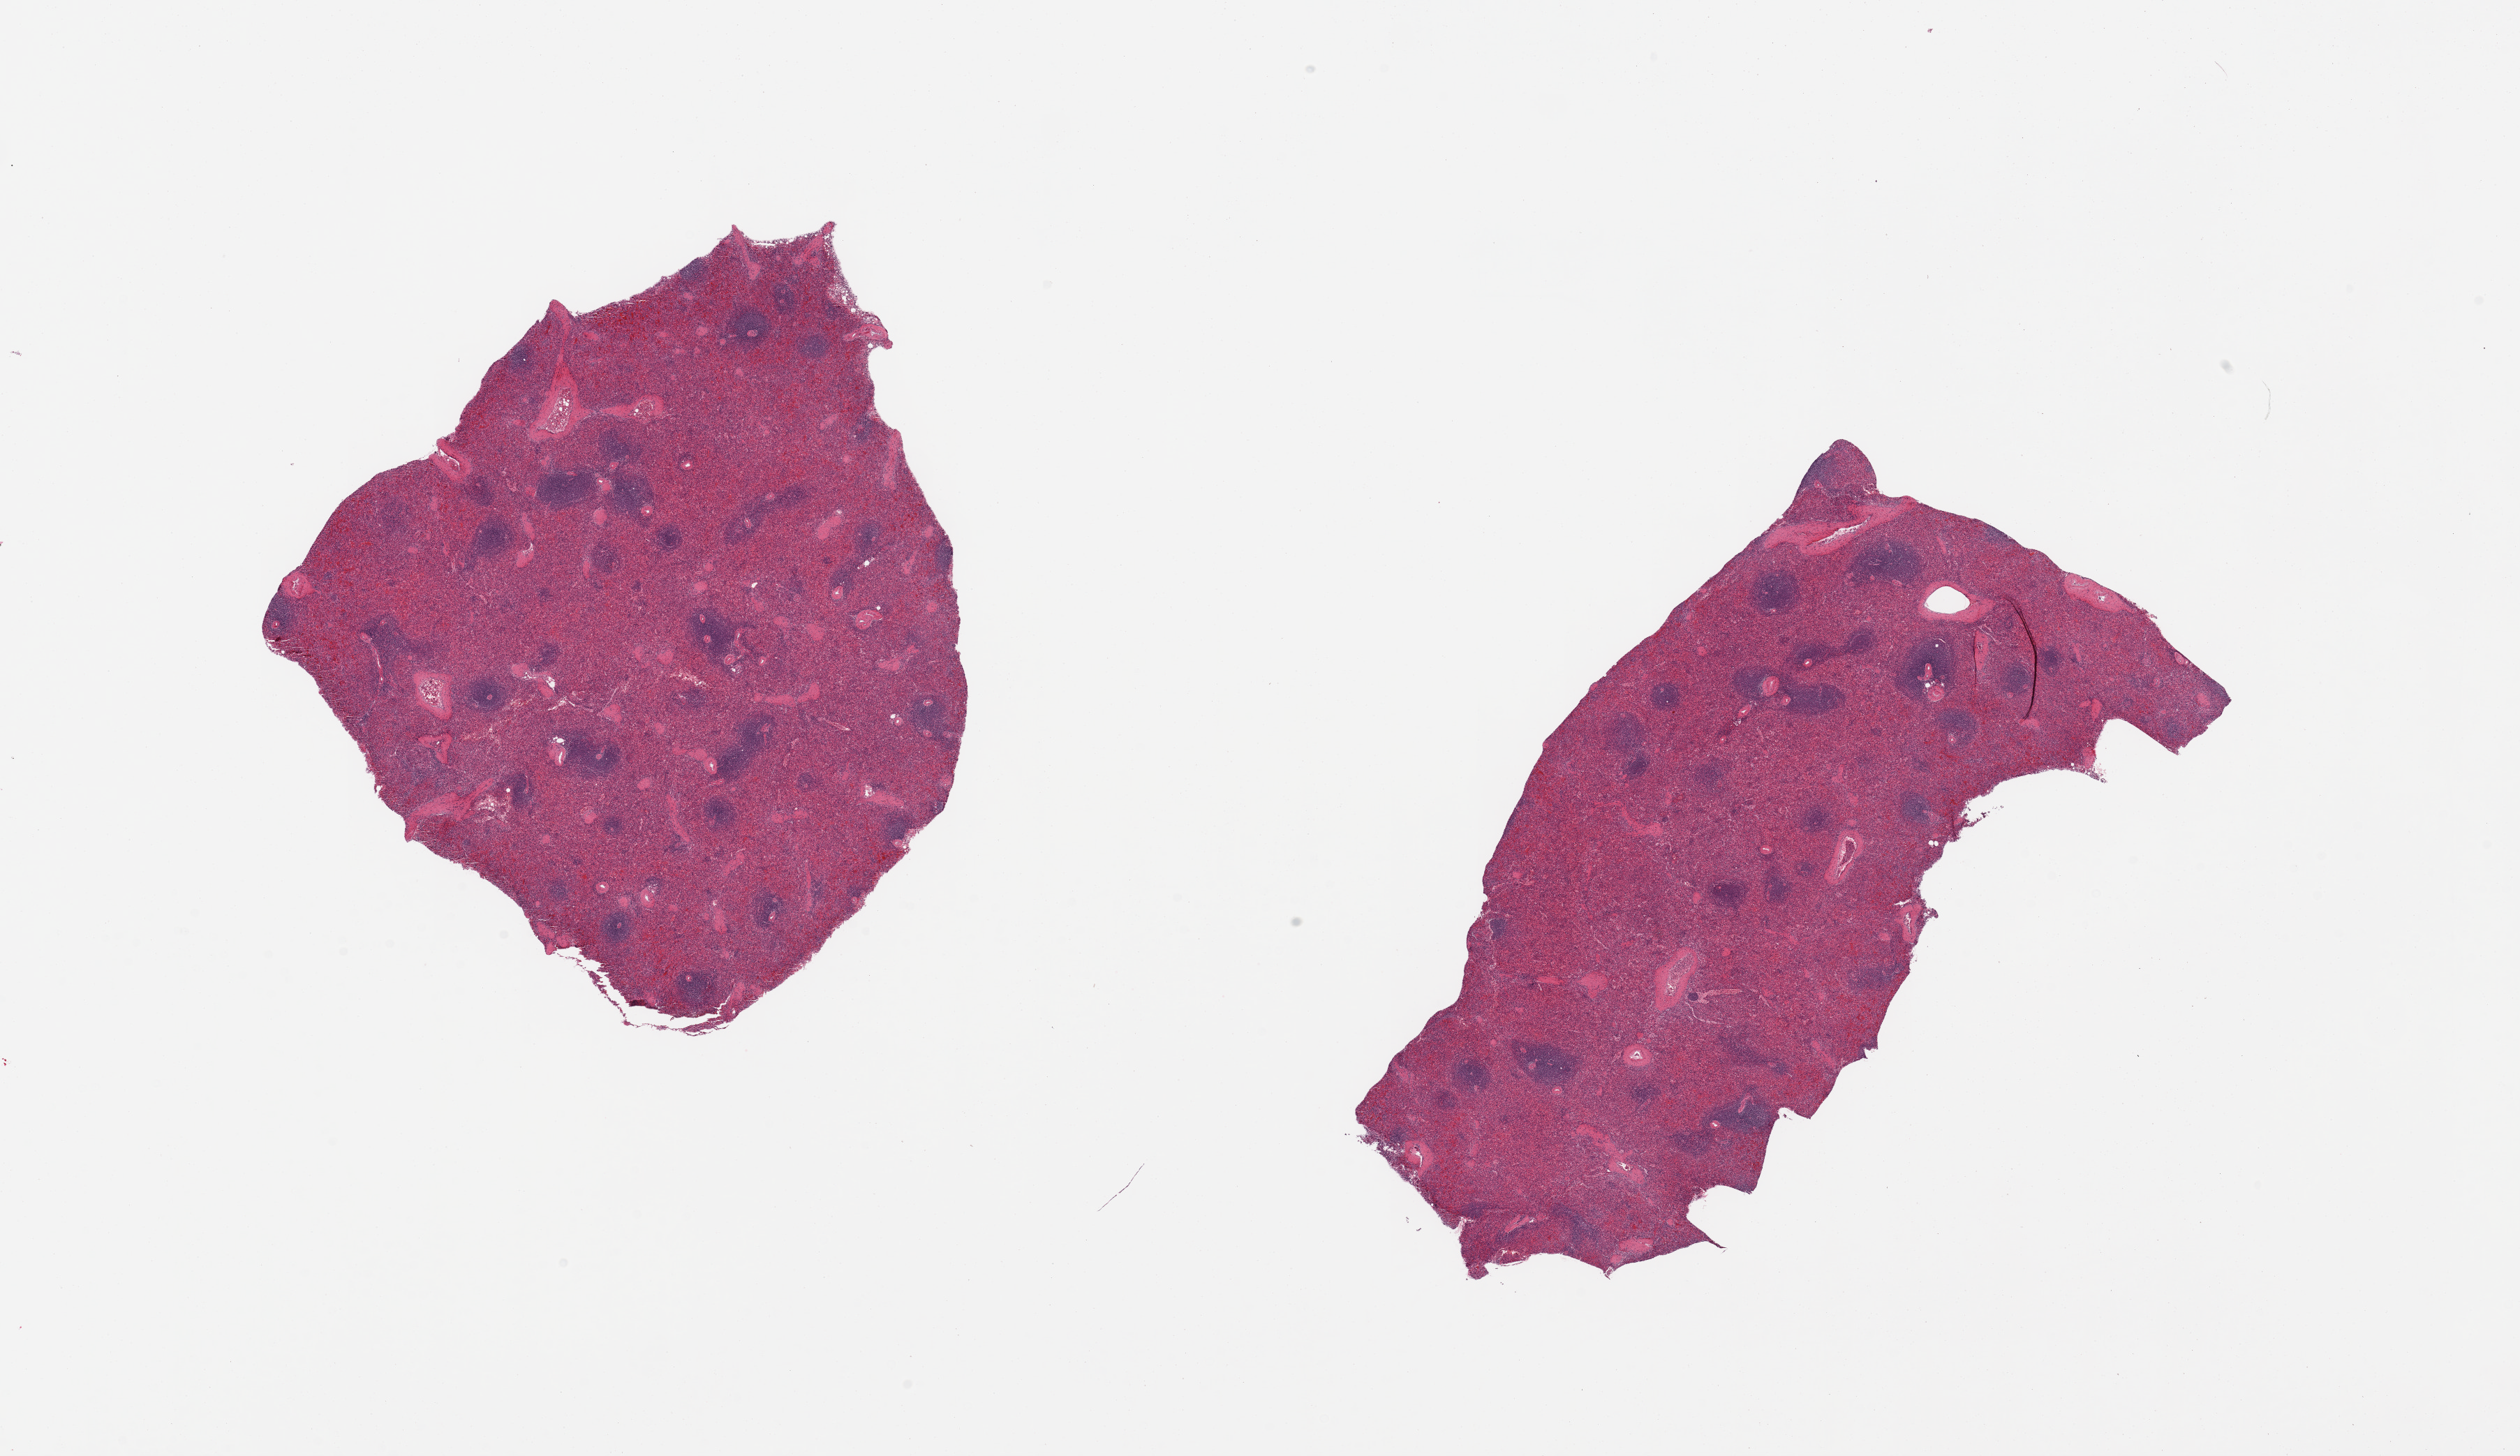
Digitized haematoxylin and eosin-stained section, brightfield — low-resolution overview of the scanned area, about 28.5 x 16.5 mm (acquisition: 20x scan). PAXgene-fixed paraffin-embedded (PFPE) section. Sampled site (target tissue): spleen. Tissue donor sample. Female donor.
Pathologist's review note for this sample: 2 pieces.